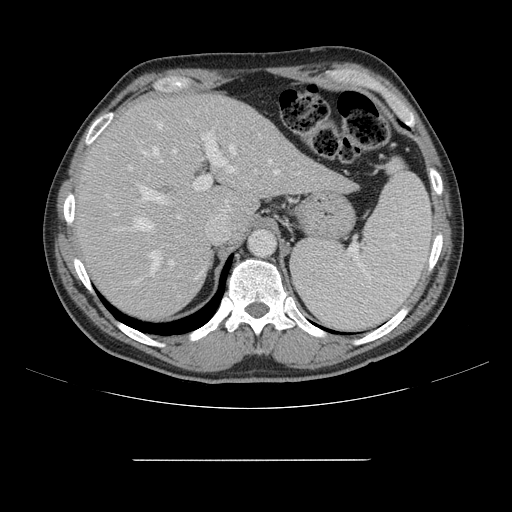
Contrast-enhanced abdominal CT, one axial slice. Position 110 of 164 along the scan axis. 120 kVp. Intravenous contrast given. Soft-tissue window (W 400 / L 40 HU). 2.5 mm slice thickness. 512 × 512 image matrix, field of view 404 × 404 mm. Male patient, age 54 years. From the clinical record (not read from this slice): diagnosis: colorectal cancer liver metastases, imaged before liver resection; multiple liver metastases: yes; largest metastasis: 1 cm; chemotherapy before resection: yes.
Annotated regions visible in this slice (expert manual segmentation):
- hepatic veins: bounding box <117,124,279,281> (left, top, right, bottom; pixels)
- liver: <77,96,350,319>
- planned liver remnant (the part of the liver to remain after resection): <77,95,243,319>
- portal vein (with intrahepatic branches): <127,123,234,286>